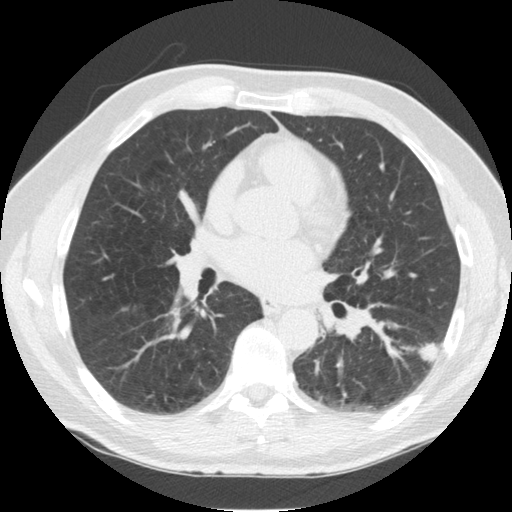
Low-dose screening chest CT, one axial slice; slice 56 of 126 in the series (ordered by position); reconstruction kernel STANDARD; lung window (W 1500 / L -600 HU); 2.5 mm slice thickness; 512 × 512 image matrix, field of view 344 × 344 mm.
Structures marked on this image (manually delineated by an expert):
- lesion 1 (tumor, lower lobe of left lung): bounding box (x1, y1, x2, y2) in pixels: (419, 343, 439, 362)